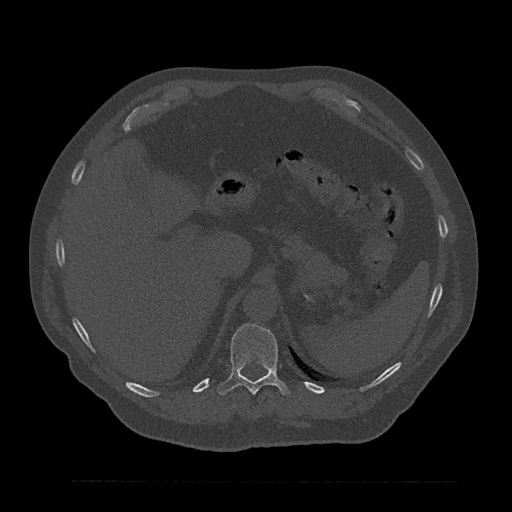
CT including the spine, one axial slice. Position 295 of 797 along the scan axis. 120 kVp. Bone window (W 1800 / L 400 HU). 512 × 512 image matrix. Patient: male, 61 years. From the clinical record (not read from this slice): primary cancer: prostate.
Structures marked on this image (semi-automatically segmented with operator editing):
- T11 vertebra: bounding box (x1, y1, x2, y2) in pixels: (217, 323, 290, 395)